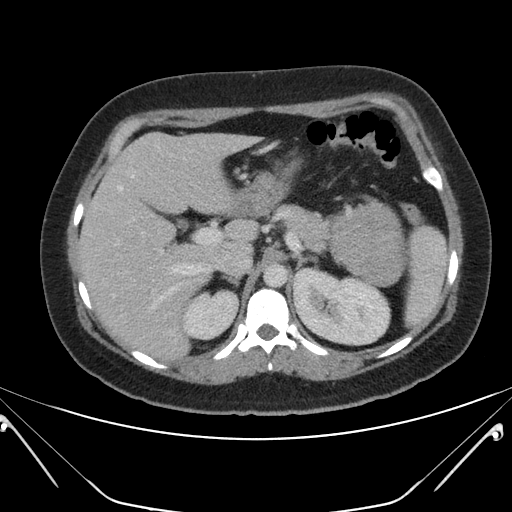
Contrast-enhanced abdominal CT, one axial slice; slice 130 of 168 in the series (ordered by position); 120 kVp; intravenous contrast given; soft-tissue window (W 400 / L 40 HU); 512 × 512 image matrix, field of view 394 × 394 mm. Patient: female, 26 years. Case-level facts recorded for this patient, not image findings: diagnosis: adrenocortical carcinoma; tumour side: left adrenal; tumour size at pathology: 28 cm; Ki-67 index: 20 %; stage (as recorded): 2.
Structures marked on this image (semi-automatically segmented with operator editing):
- mass: bounding box <332,203,404,286> (left, top, right, bottom; pixels)